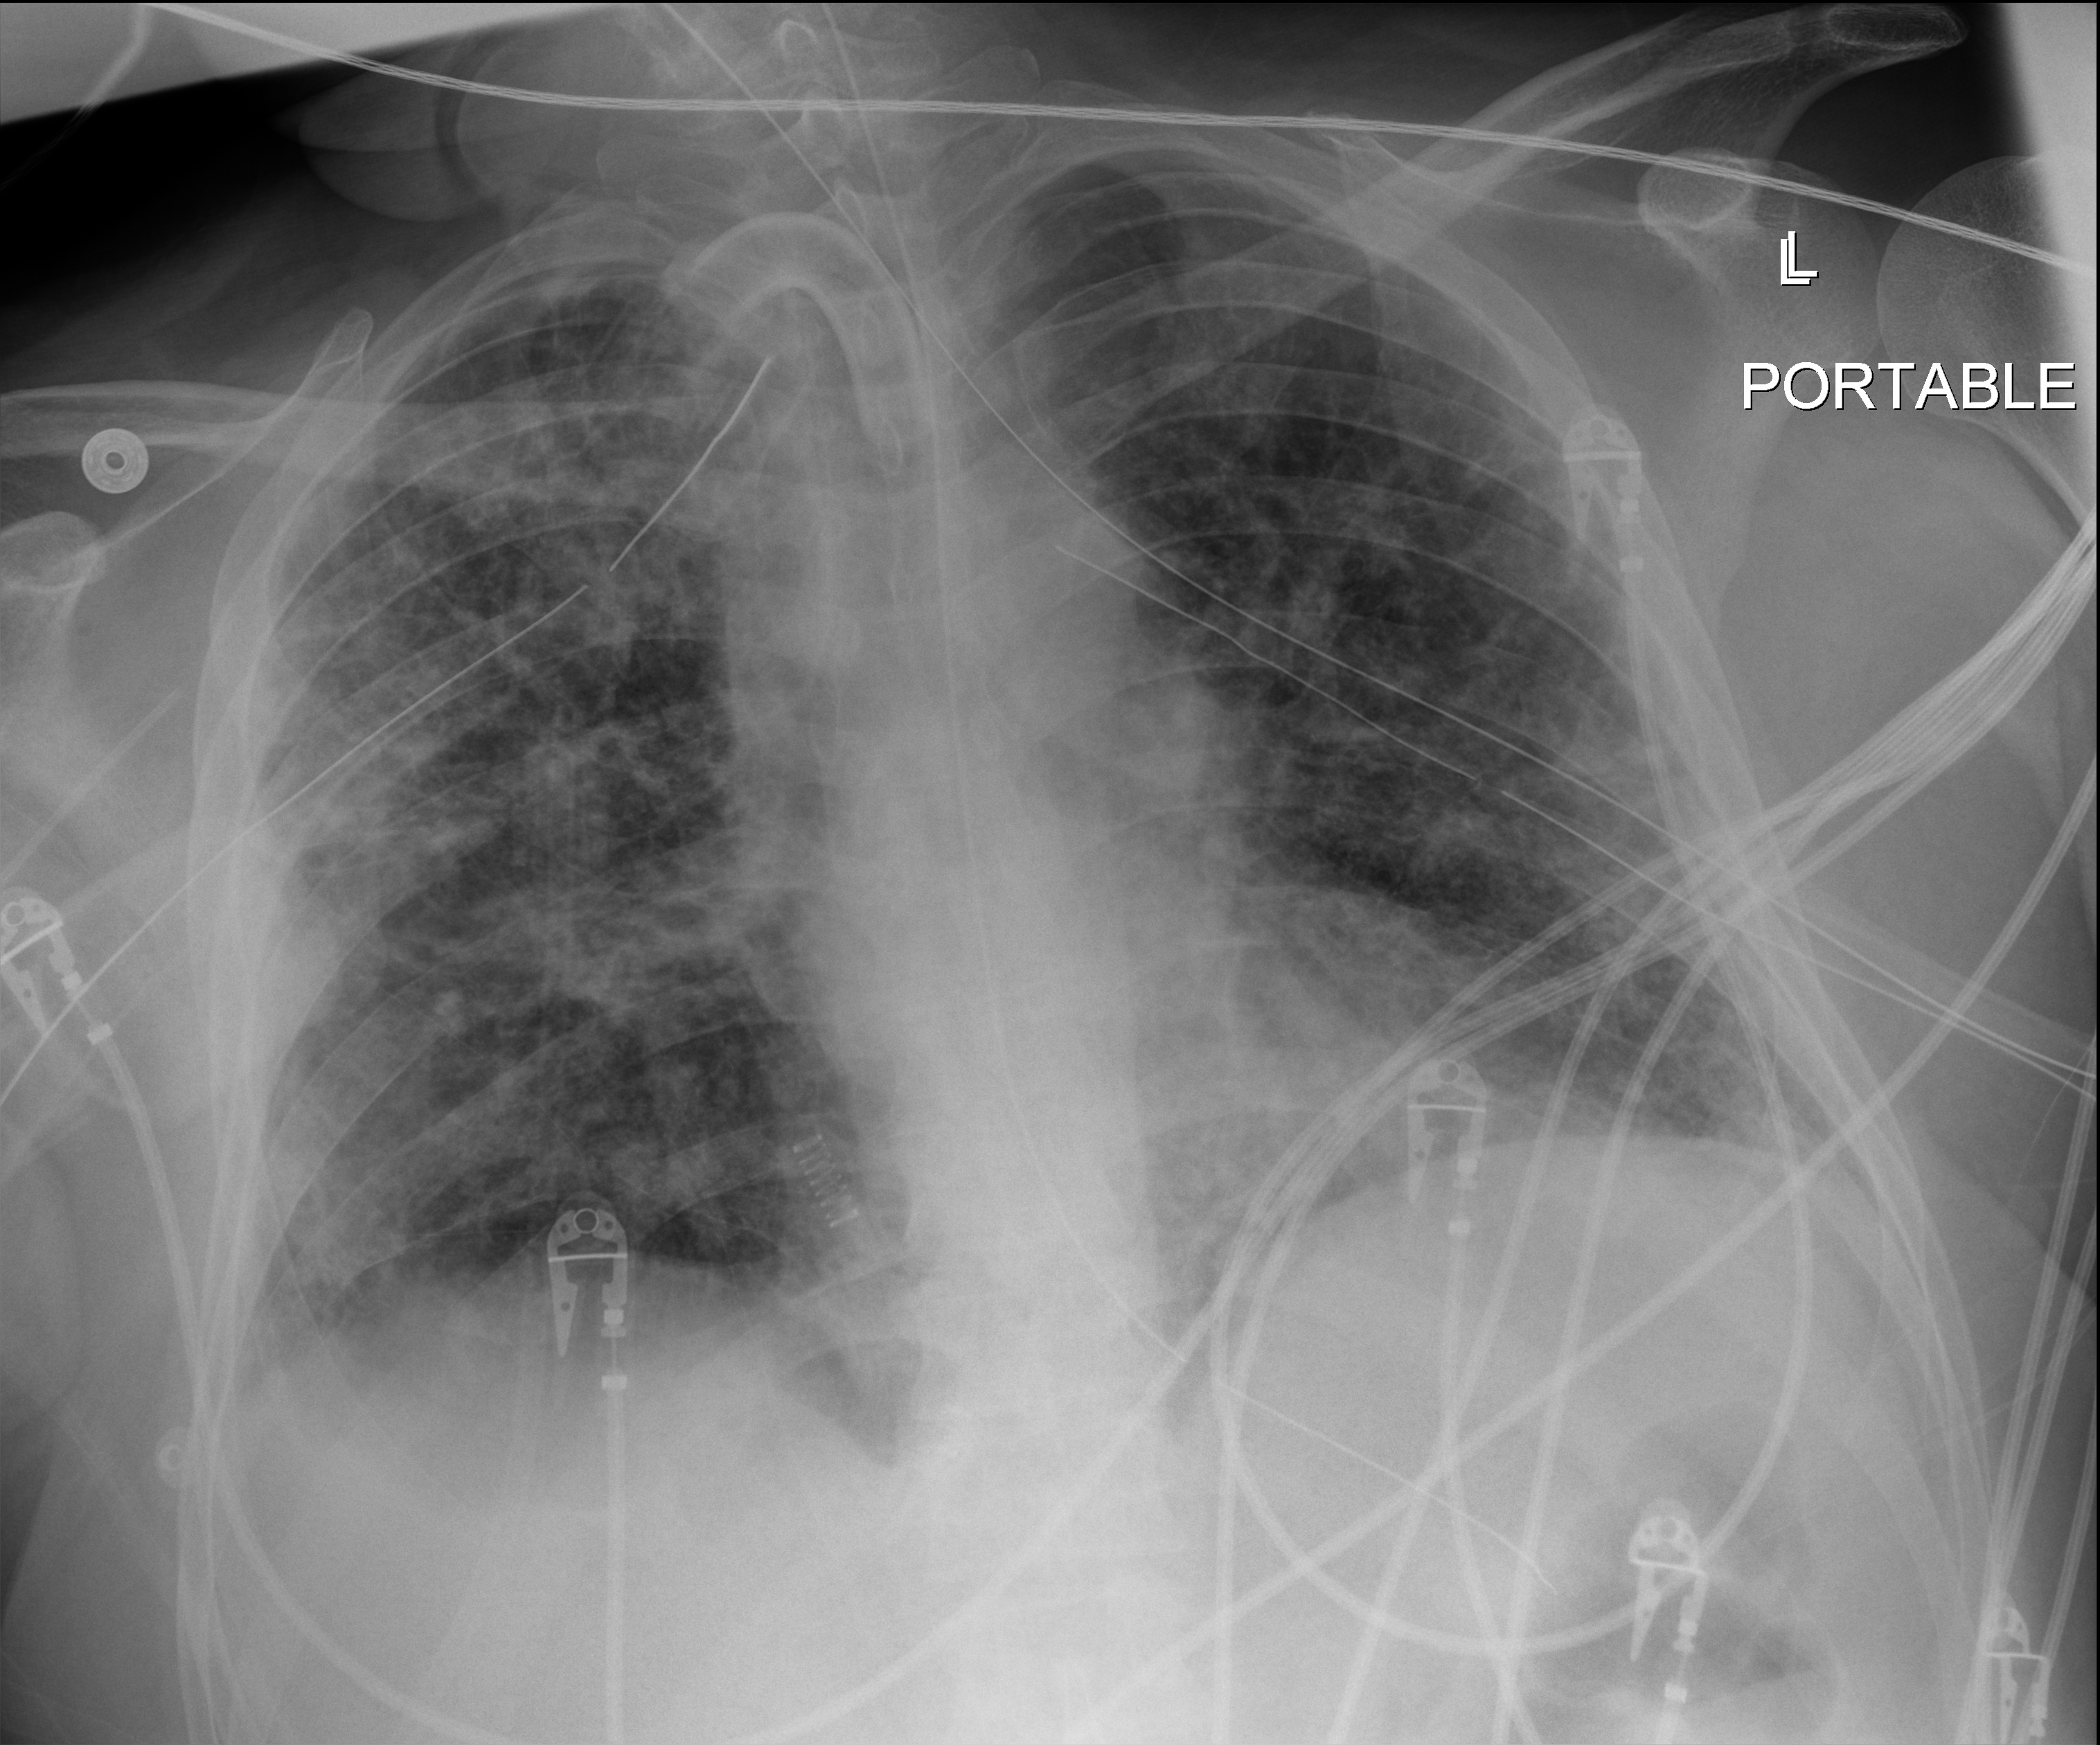
Chest X-ray, anteroposterior (AP) projection. Male patient hospitalised with COVID-19, age 18–59 years.
Admission-level facts for this patient (not findings on this image; timing relative to this image not recorded): COPD (admission record): no; length of hospital stay: 63 days.